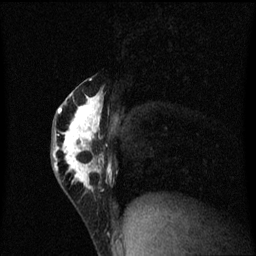
Breast MRI (dynamic contrast-enhanced), one sagittal slice. Position 29 of 60 along the scan axis. Dynamic contrast-enhanced series, image 2 of 3 at this slice position (ordered by acquisition). 1.5 T. TE 4.2 ms, TR 8.4 ms. 2 mm slice thickness. 256 × 256 image matrix. Female patient, age 40 years.
Annotated regions visible in this slice (semi-automatically segmented with operator editing):
- analysis volume of interest (the breast-tissue region the enhancement analysis was run in; not a lesion): bounding box (x1, y1, x2, y2) in pixels: (52, 76, 111, 201)
- tumour enhancement mask (voxels above the 70 % enhancement threshold inside the analysis volume of interest): (54, 78, 111, 189)